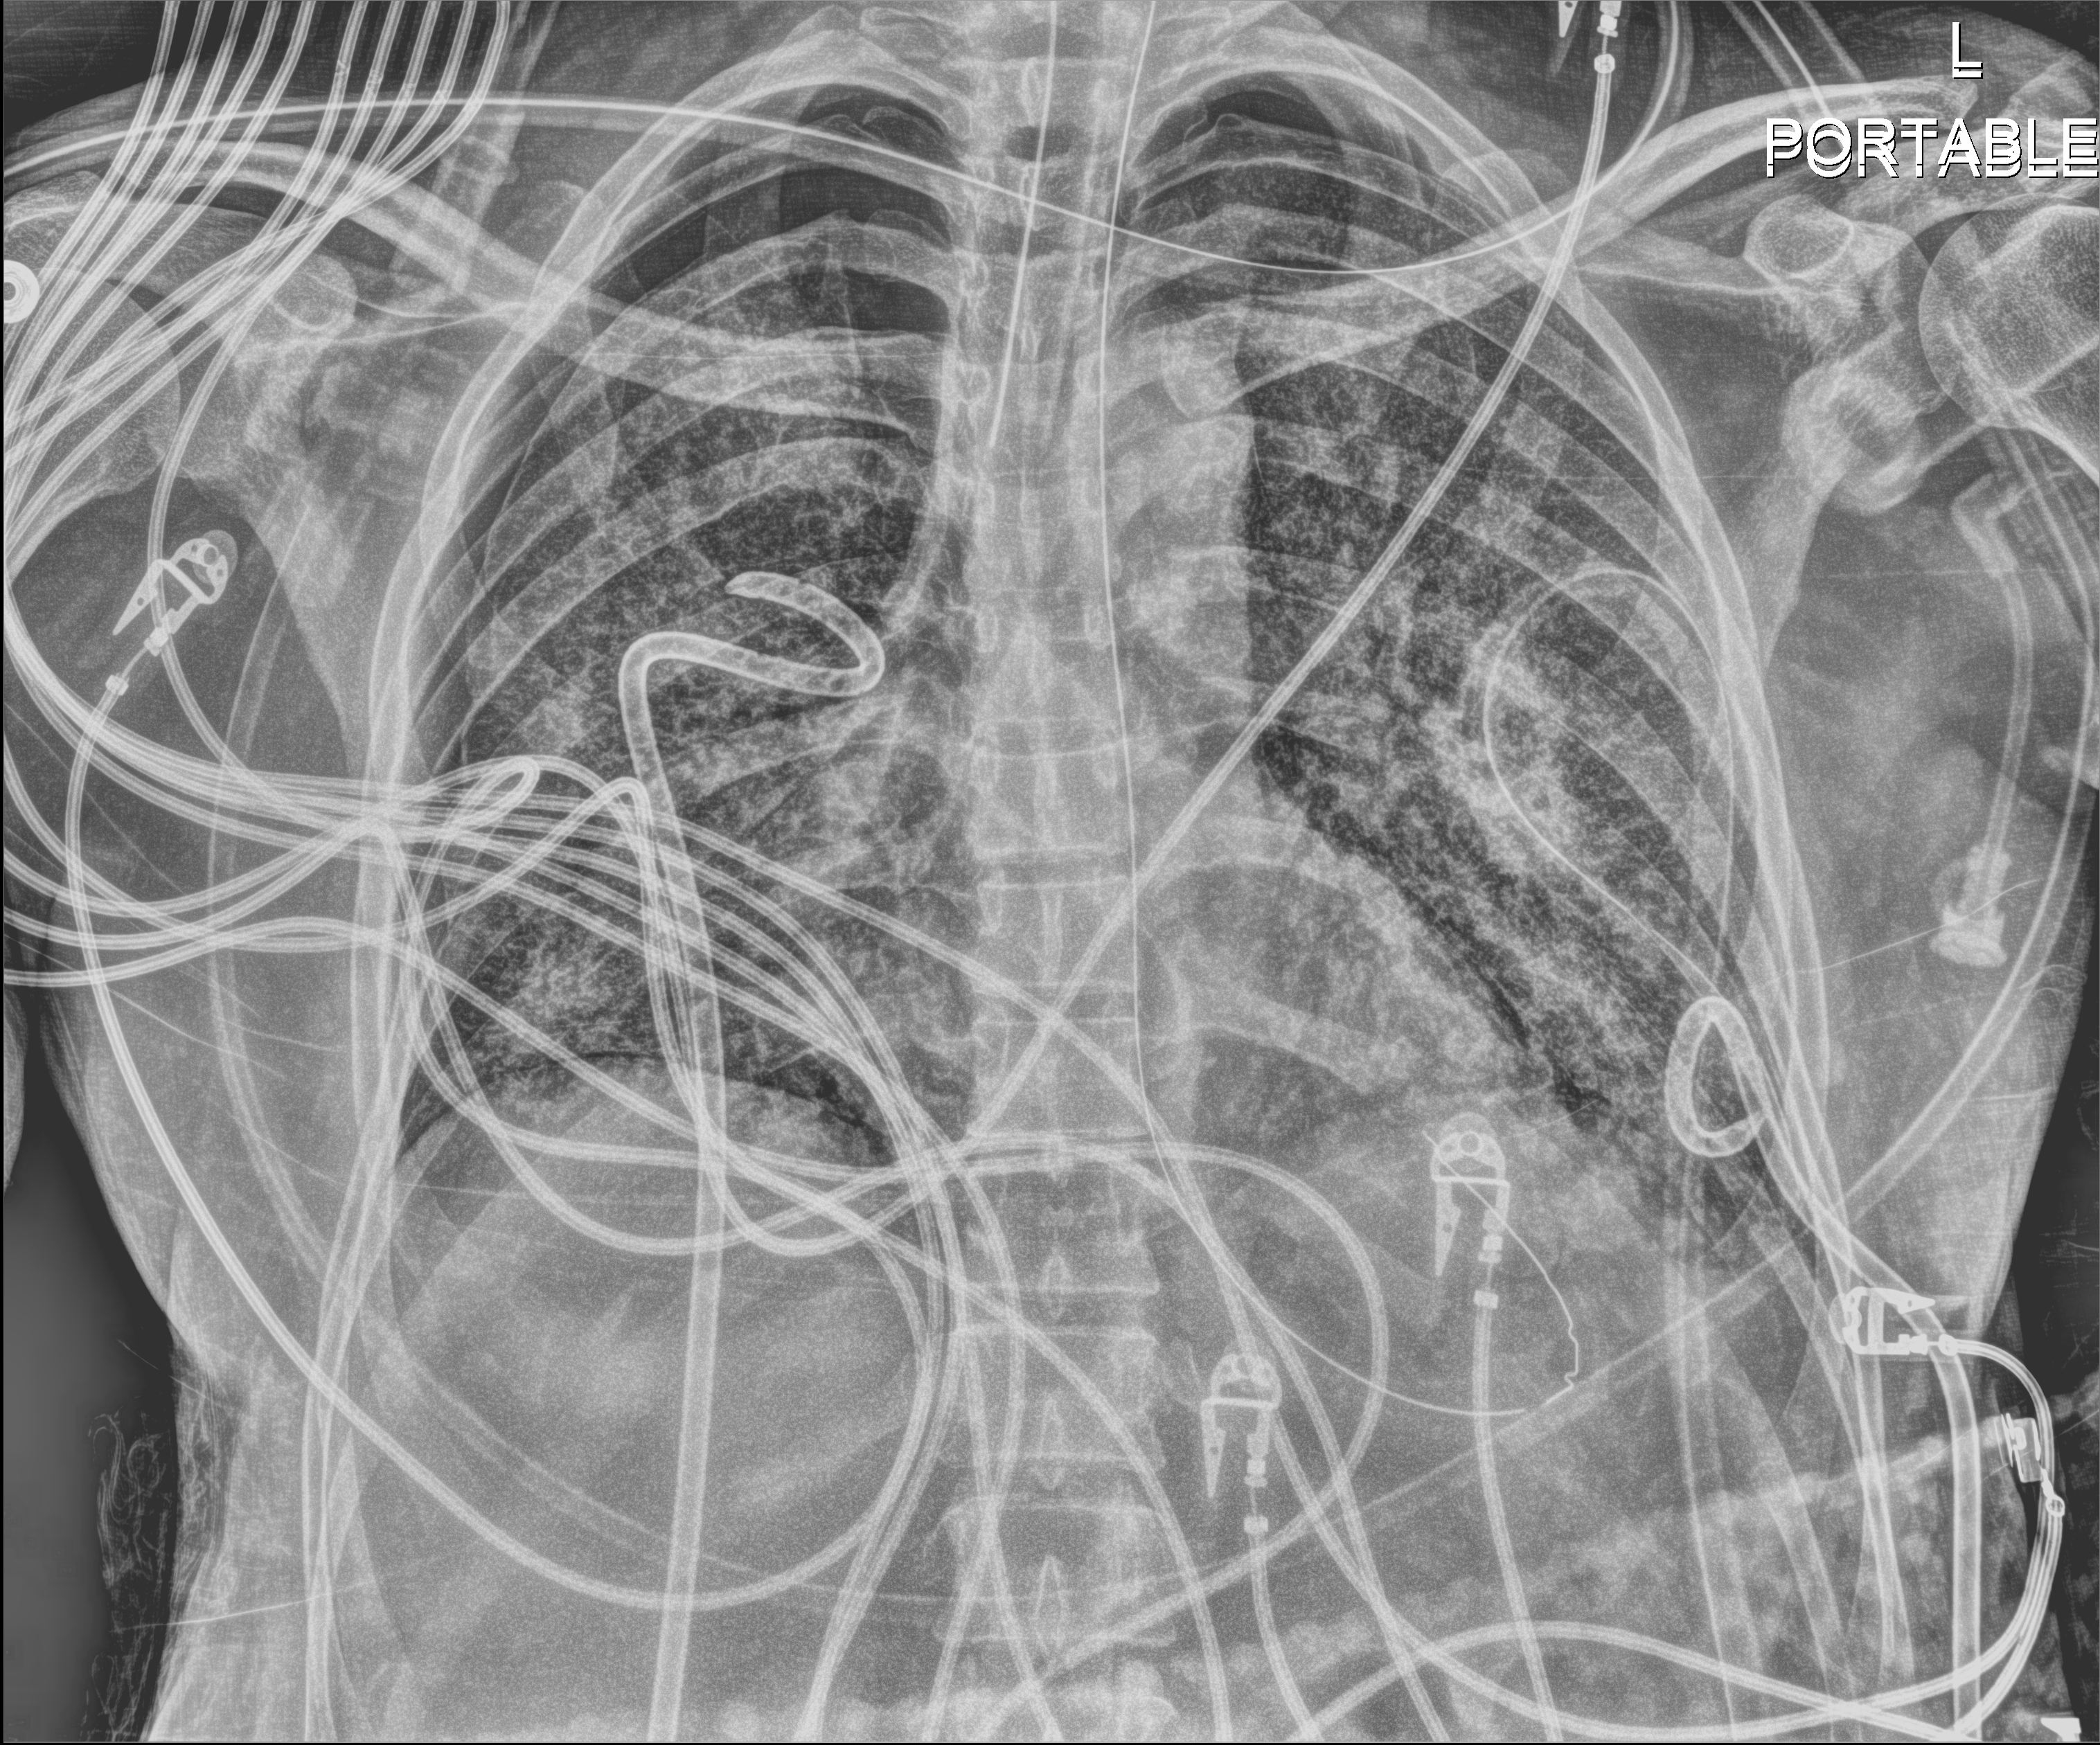
Chest radiograph; anteroposterior (AP) projection. Adult patient hospitalised with COVID-19, age 18–59 years.
Admission-level facts for this patient (not findings on this image; timing relative to this image not recorded): chronic kidney disease (admission record): no.